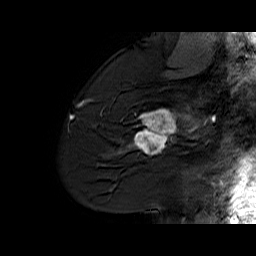
Breast MRI (dynamic contrast-enhanced), one sagittal slice; position 44 of 60 along the scan axis; dynamic contrast-enhanced series, time point 2 of 6 at this slice position (early post-contrast); 1.5 T; TE 6.1 ms, TR 32.9 ms; 4 mm slice thickness; 256 × 256 image matrix. Female patient. From the clinical record (not read from this slice): setting: breast cancer imaged before/during neoadjuvant chemotherapy; receptor status: HER2-positive.
Structures marked on this image (semi-automatically segmented with operator editing):
- analysis volume of interest (the breast-tissue region the enhancement analysis was run in; not a lesion): bounding box [x1, y1, x2, y2] px = [127, 95, 194, 165]
- tumour enhancement mask (voxels above the 100 % enhancement threshold inside the analysis volume of interest): [128, 109, 194, 154]